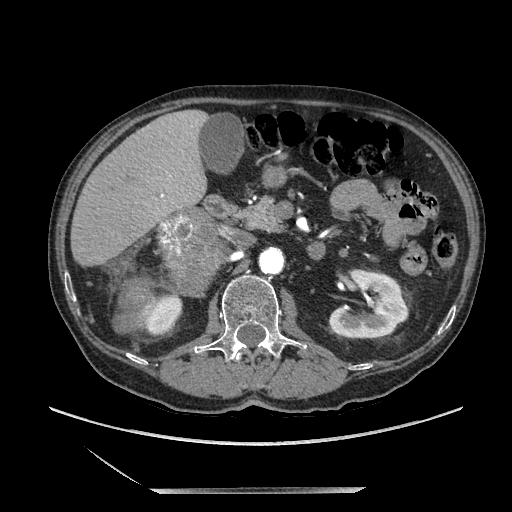
Contrast-enhanced abdominal CT, one axial slice; position 100 of 243 along the scan axis; soft-tissue window (W 400 / L 40 HU); 1.25 mm slice thickness; 512 × 512 image matrix, field of view 420 × 420 mm. Male patient. Case-level facts recorded for this patient, not image findings: diagnosis: adrenocortical carcinoma; tumour side: right adrenal; tumour size at pathology: 16 cm; Ki-67 index: 17 %; stage (as recorded): 3.
Outlined on this slice (semi-automatically segmented with operator editing):
- mass: bounding box [x1, y1, x2, y2] px = [163, 208, 218, 291]